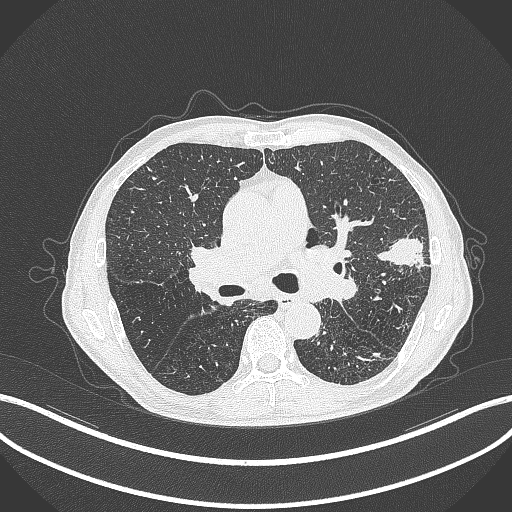
Chest CT, one axial slice. Slice 249 of 463 in the series (ordered by position). Lung window (W 1500 / L -600 HU). 512 × 512 image matrix, field of view 400 × 400 mm. Male patient, age 74 years. Case-level facts recorded for this patient, not image findings: clinical TNM (as recorded): T2a N1 M0.
Outlined on this slice (rectangle marked by the reading radiologist):
- lung tumour (recorded histology: adenocarcinoma): bounding box [x1, y1, x2, y2] px = [376, 233, 433, 273]